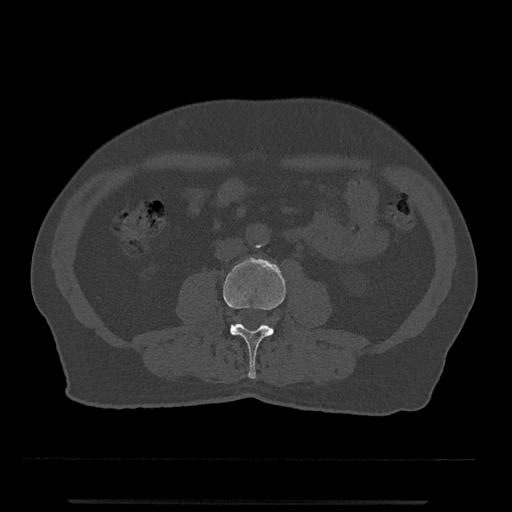
CT including the spine, one axial slice. Slice 191 of 797 in the series (ordered by position). Reconstruction kernel Br40s/3. 120 kVp. Bone window (W 1800 / L 400 HU). 0.5 mm slice thickness. 512 × 512 image matrix, field of view 419 × 419 mm. Male patient, age 63 years. From the clinical record (not read from this slice): primary cancer: prostate.
Annotated regions visible in this slice (semi-automatically segmented with operator editing):
- L3 vertebra: bounding box <223,257,286,379> (left, top, right, bottom; pixels)